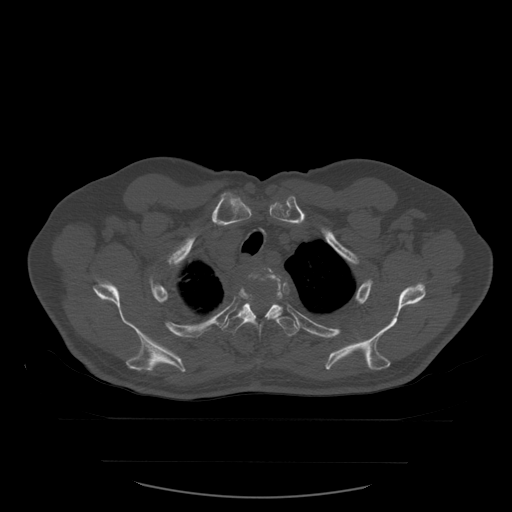
CT including the spine, one axial slice. Slice 452 of 590 in the series (ordered by position). Bone window (W 1800 / L 400 HU). 512 × 512 image matrix. Patient age 71 years. Case-level facts recorded for this patient, not image findings: primary cancer: lung.
Outlined on this slice (semi-automatic segmentation, software-assisted and operator-edited):
- T2 vertebra: bounding box <267,269,281,280> (left, top, right, bottom; pixels)
- T3 vertebra: <239,274,283,317>
- T4 vertebra: <222,294,300,342>
- T5 vertebra: <265,318,270,321>